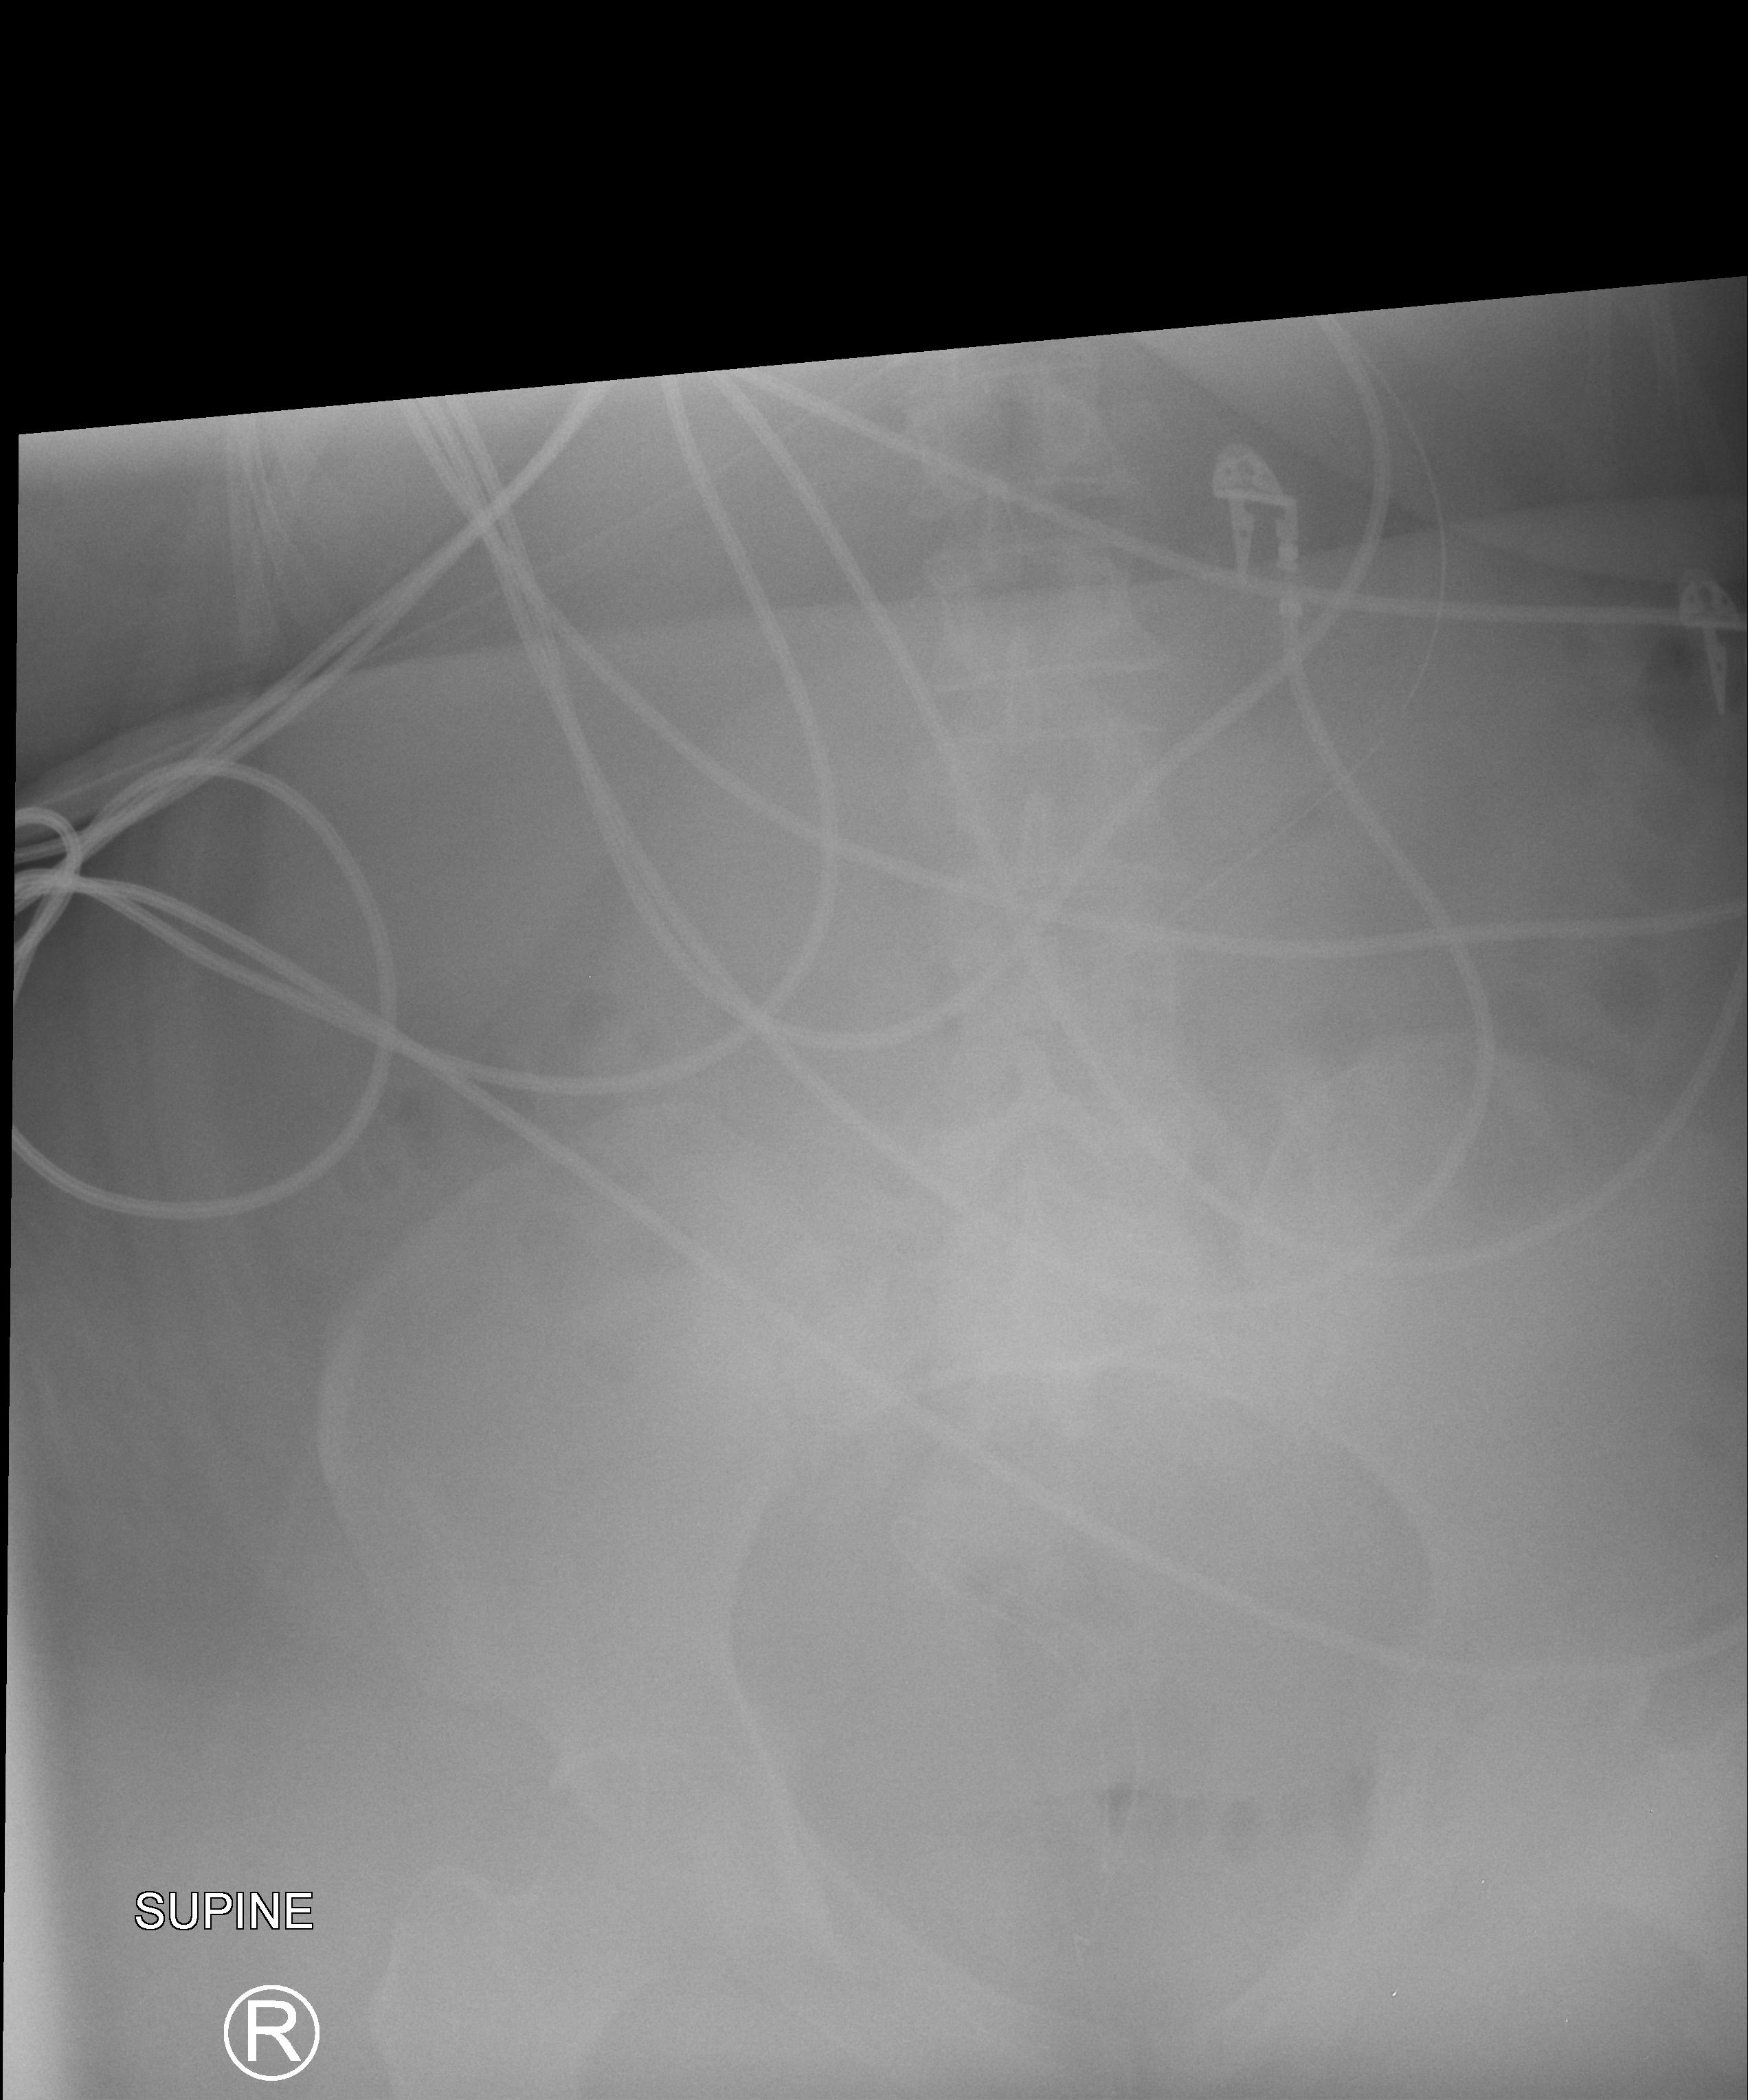
Abdomen X-ray (portable). Patient hospitalised with COVID-19; female, aged 18–59 years.
Admission-level facts for this patient (not findings on this image; timing relative to this image not recorded): admitted to intensive care during this hospital stay: yes; chronic kidney disease (admission record): no.